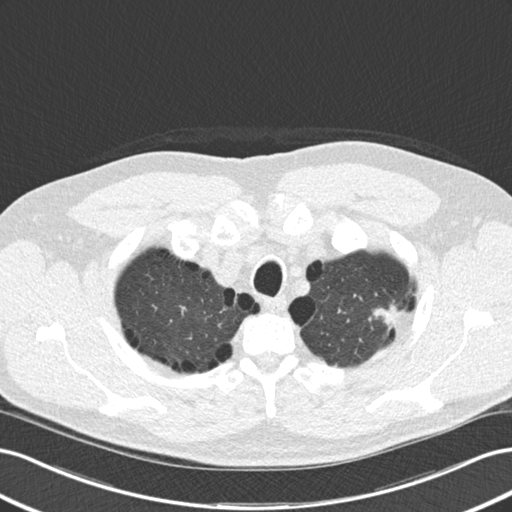
Low-dose screening chest CT, one axial slice; slice 144 of 177 in the series (ordered by position); 120 kVp; lung window (W 1500 / L -600 HU); 2 mm slice thickness; 512 × 512 image matrix, field of view 360 × 360 mm.
Outlined on this slice (expert manual segmentation):
- lesion 1 (tumor, upper lobe of left lung): bounding box <374,303,400,330> (left, top, right, bottom; pixels)